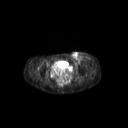
FDG PET of an extremity soft-tissue mass (from a PET/CT study), one axial slice; slice 74 of 267 in the series (ordered by position); 3.27 mm slice thickness; 128 × 128 image matrix, field of view 600 × 600 mm. Patient: female, 24 years. From the clinical record (not read from this slice): histological type: leiomyosarcoma; grade: high; site of the primary tumour: groin.
Annotated regions visible in this slice (expert contour drawn on MRI and transferred to this co-registered scan by the dataset authors):
- gross tumour volume including surrounding oedema: bounding box [x1, y1, x2, y2] px = [69, 52, 92, 64]
- gross tumour volume (mass): [69, 52, 82, 64]